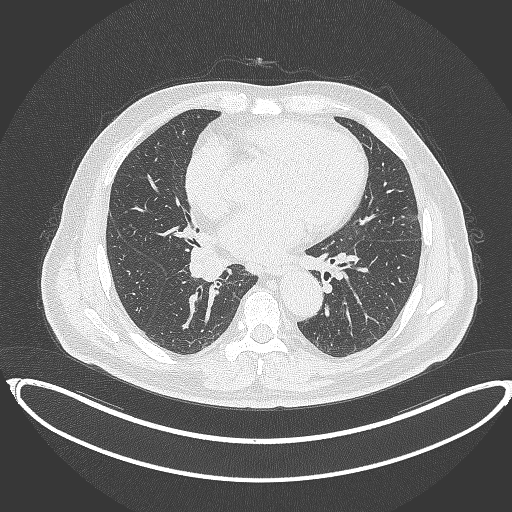
Chest CT, one axial slice; position 192 of 387 along the scan axis; reconstruction kernel B70f; 120 kVp; lung window (W 1500 / L -600 HU); 1 mm slice thickness; 512 × 512 image matrix, field of view 448 × 448 mm. Male patient, age 61 years. From the clinical record (not read from this slice): clinical TNM (as recorded): T1b N1 M0.
Structures marked on this image (bounding box drawn by a radiologist):
- lung tumour (recorded histology: squamous cell carcinoma): bounding box <185,245,229,284> (left, top, right, bottom; pixels)